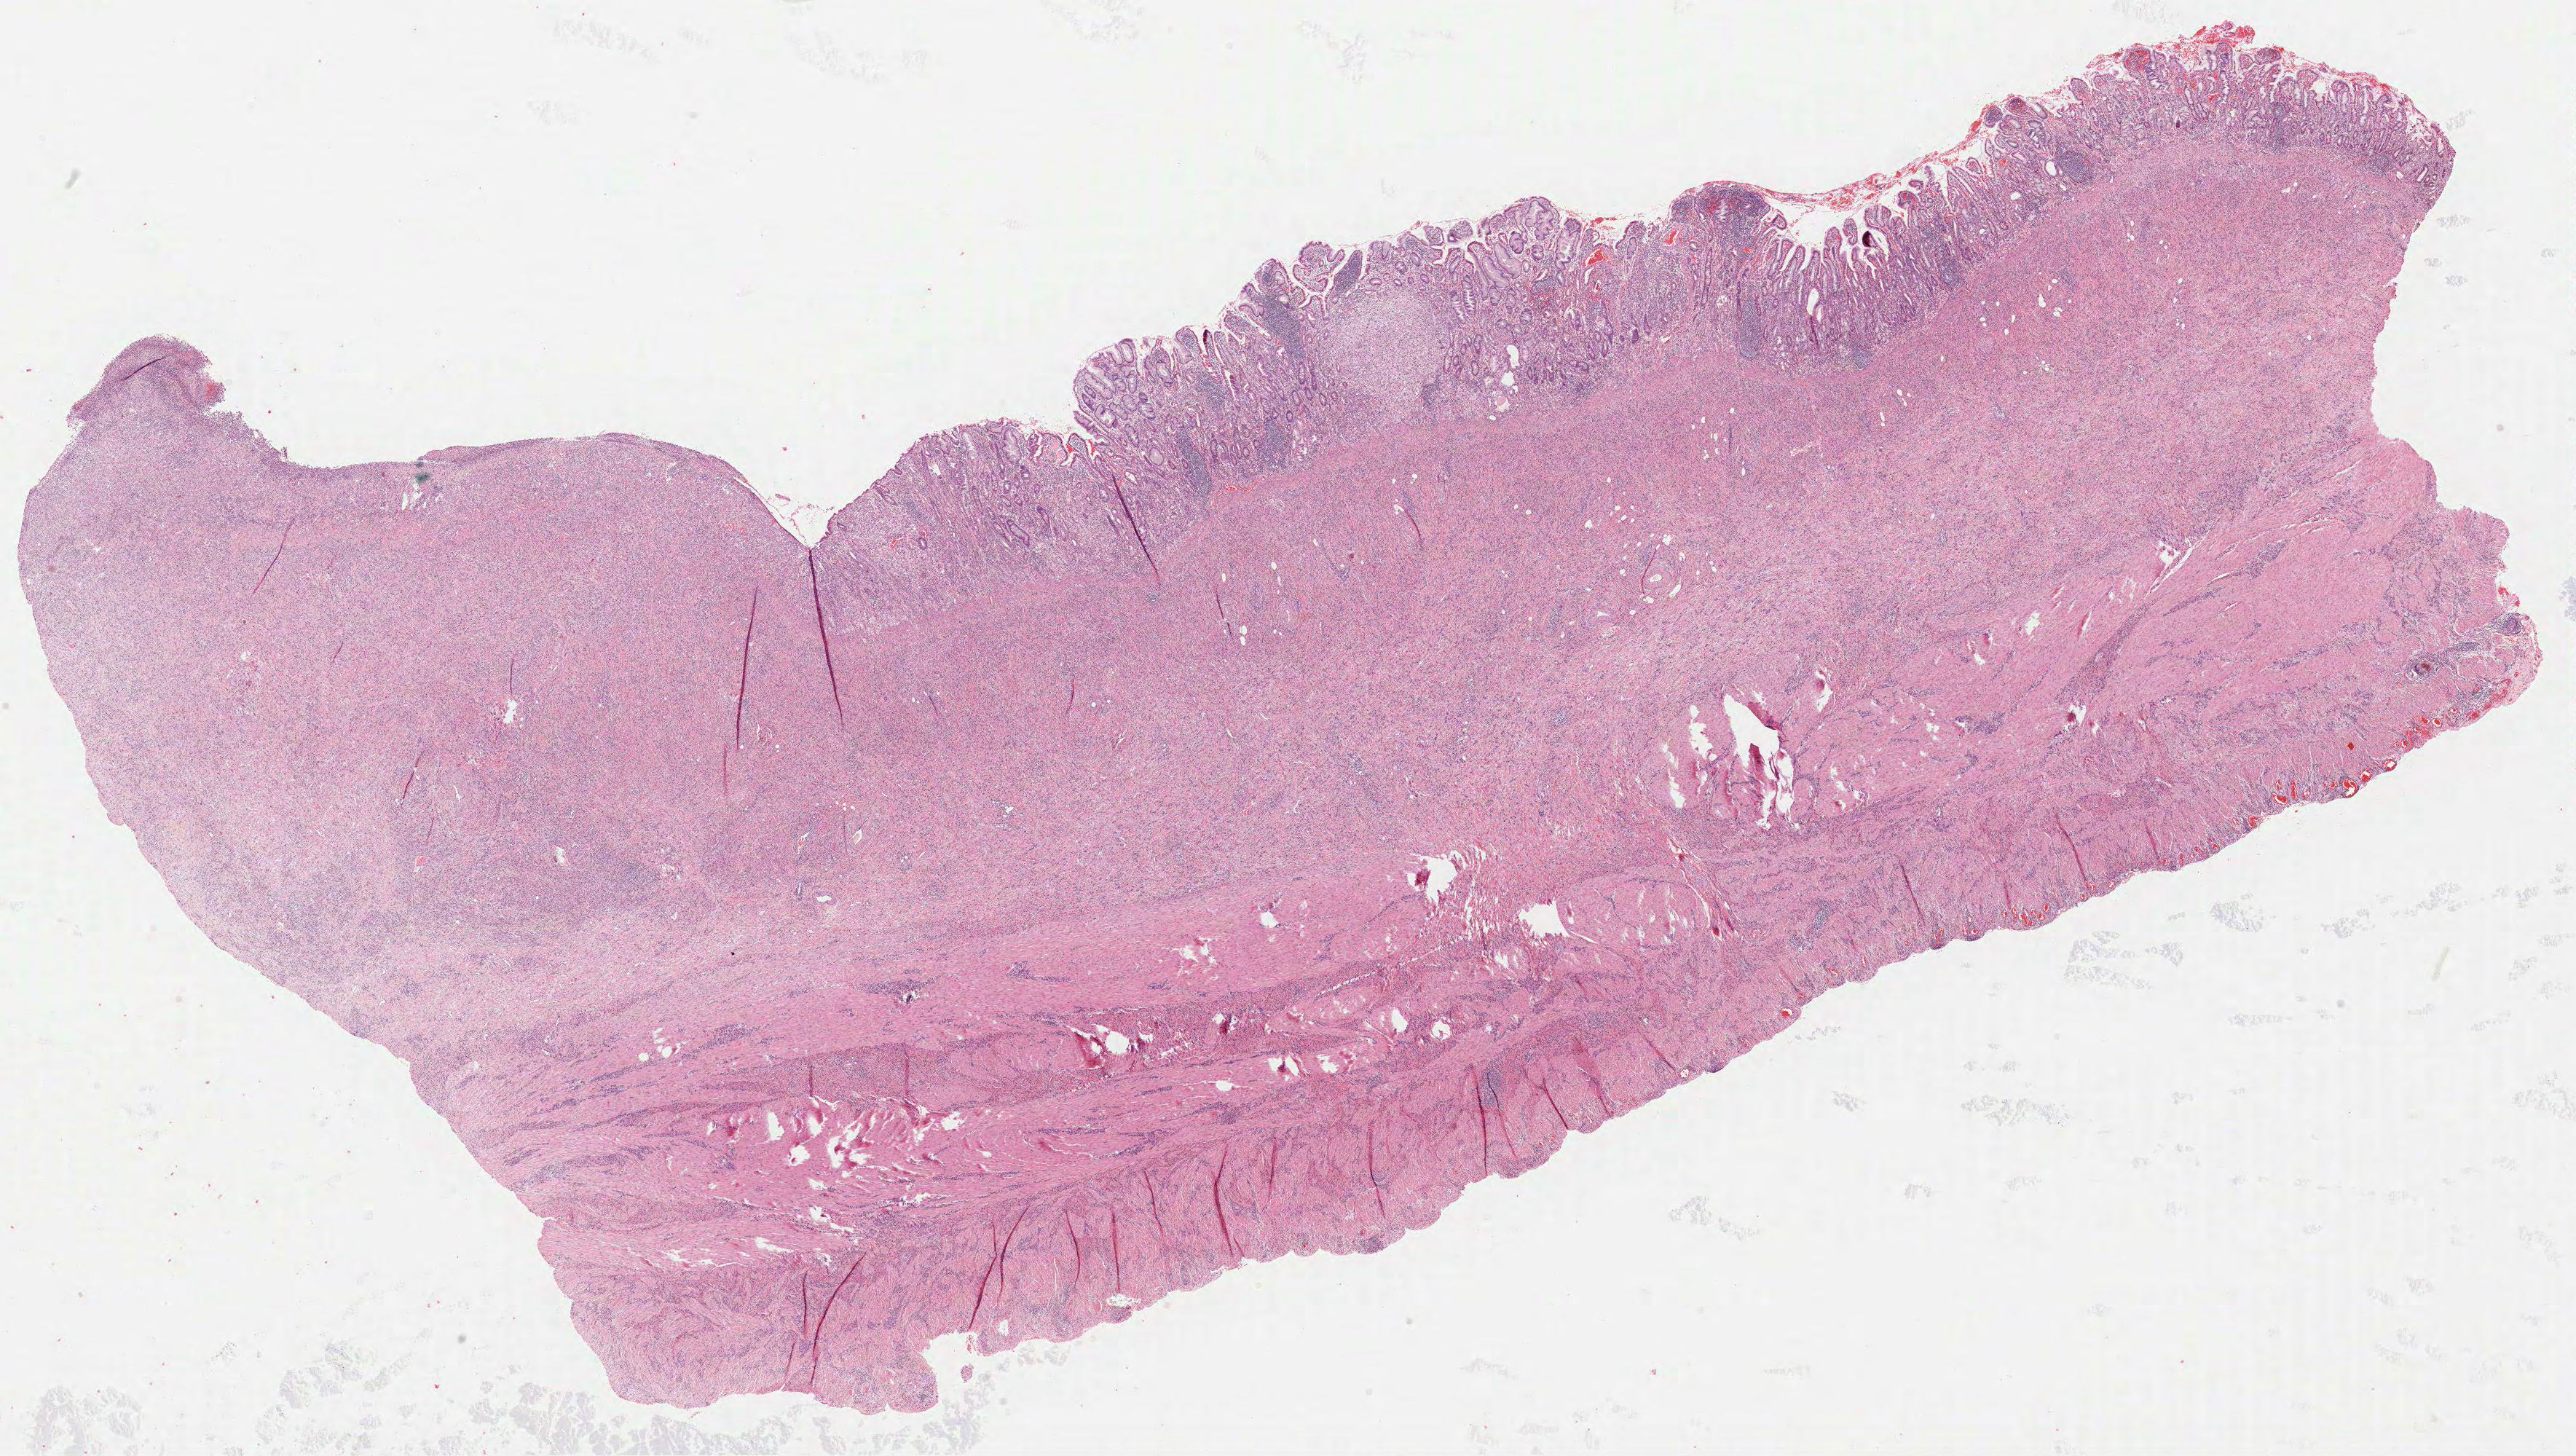
Digitized Hematoxylin and eosin (H&E) stained tissue section (whole slide), low-resolution overview of the scanned area, about 28.5 x 16.1 mm. Formalin-fixed paraffin-embedded (FFPE) diagnostic section. Sample: primary tumour, stomach. Female patient; age at initial diagnosis 46 years.
Histologic diagnosis: Adenocarcinoma, NOS (body of stomach).